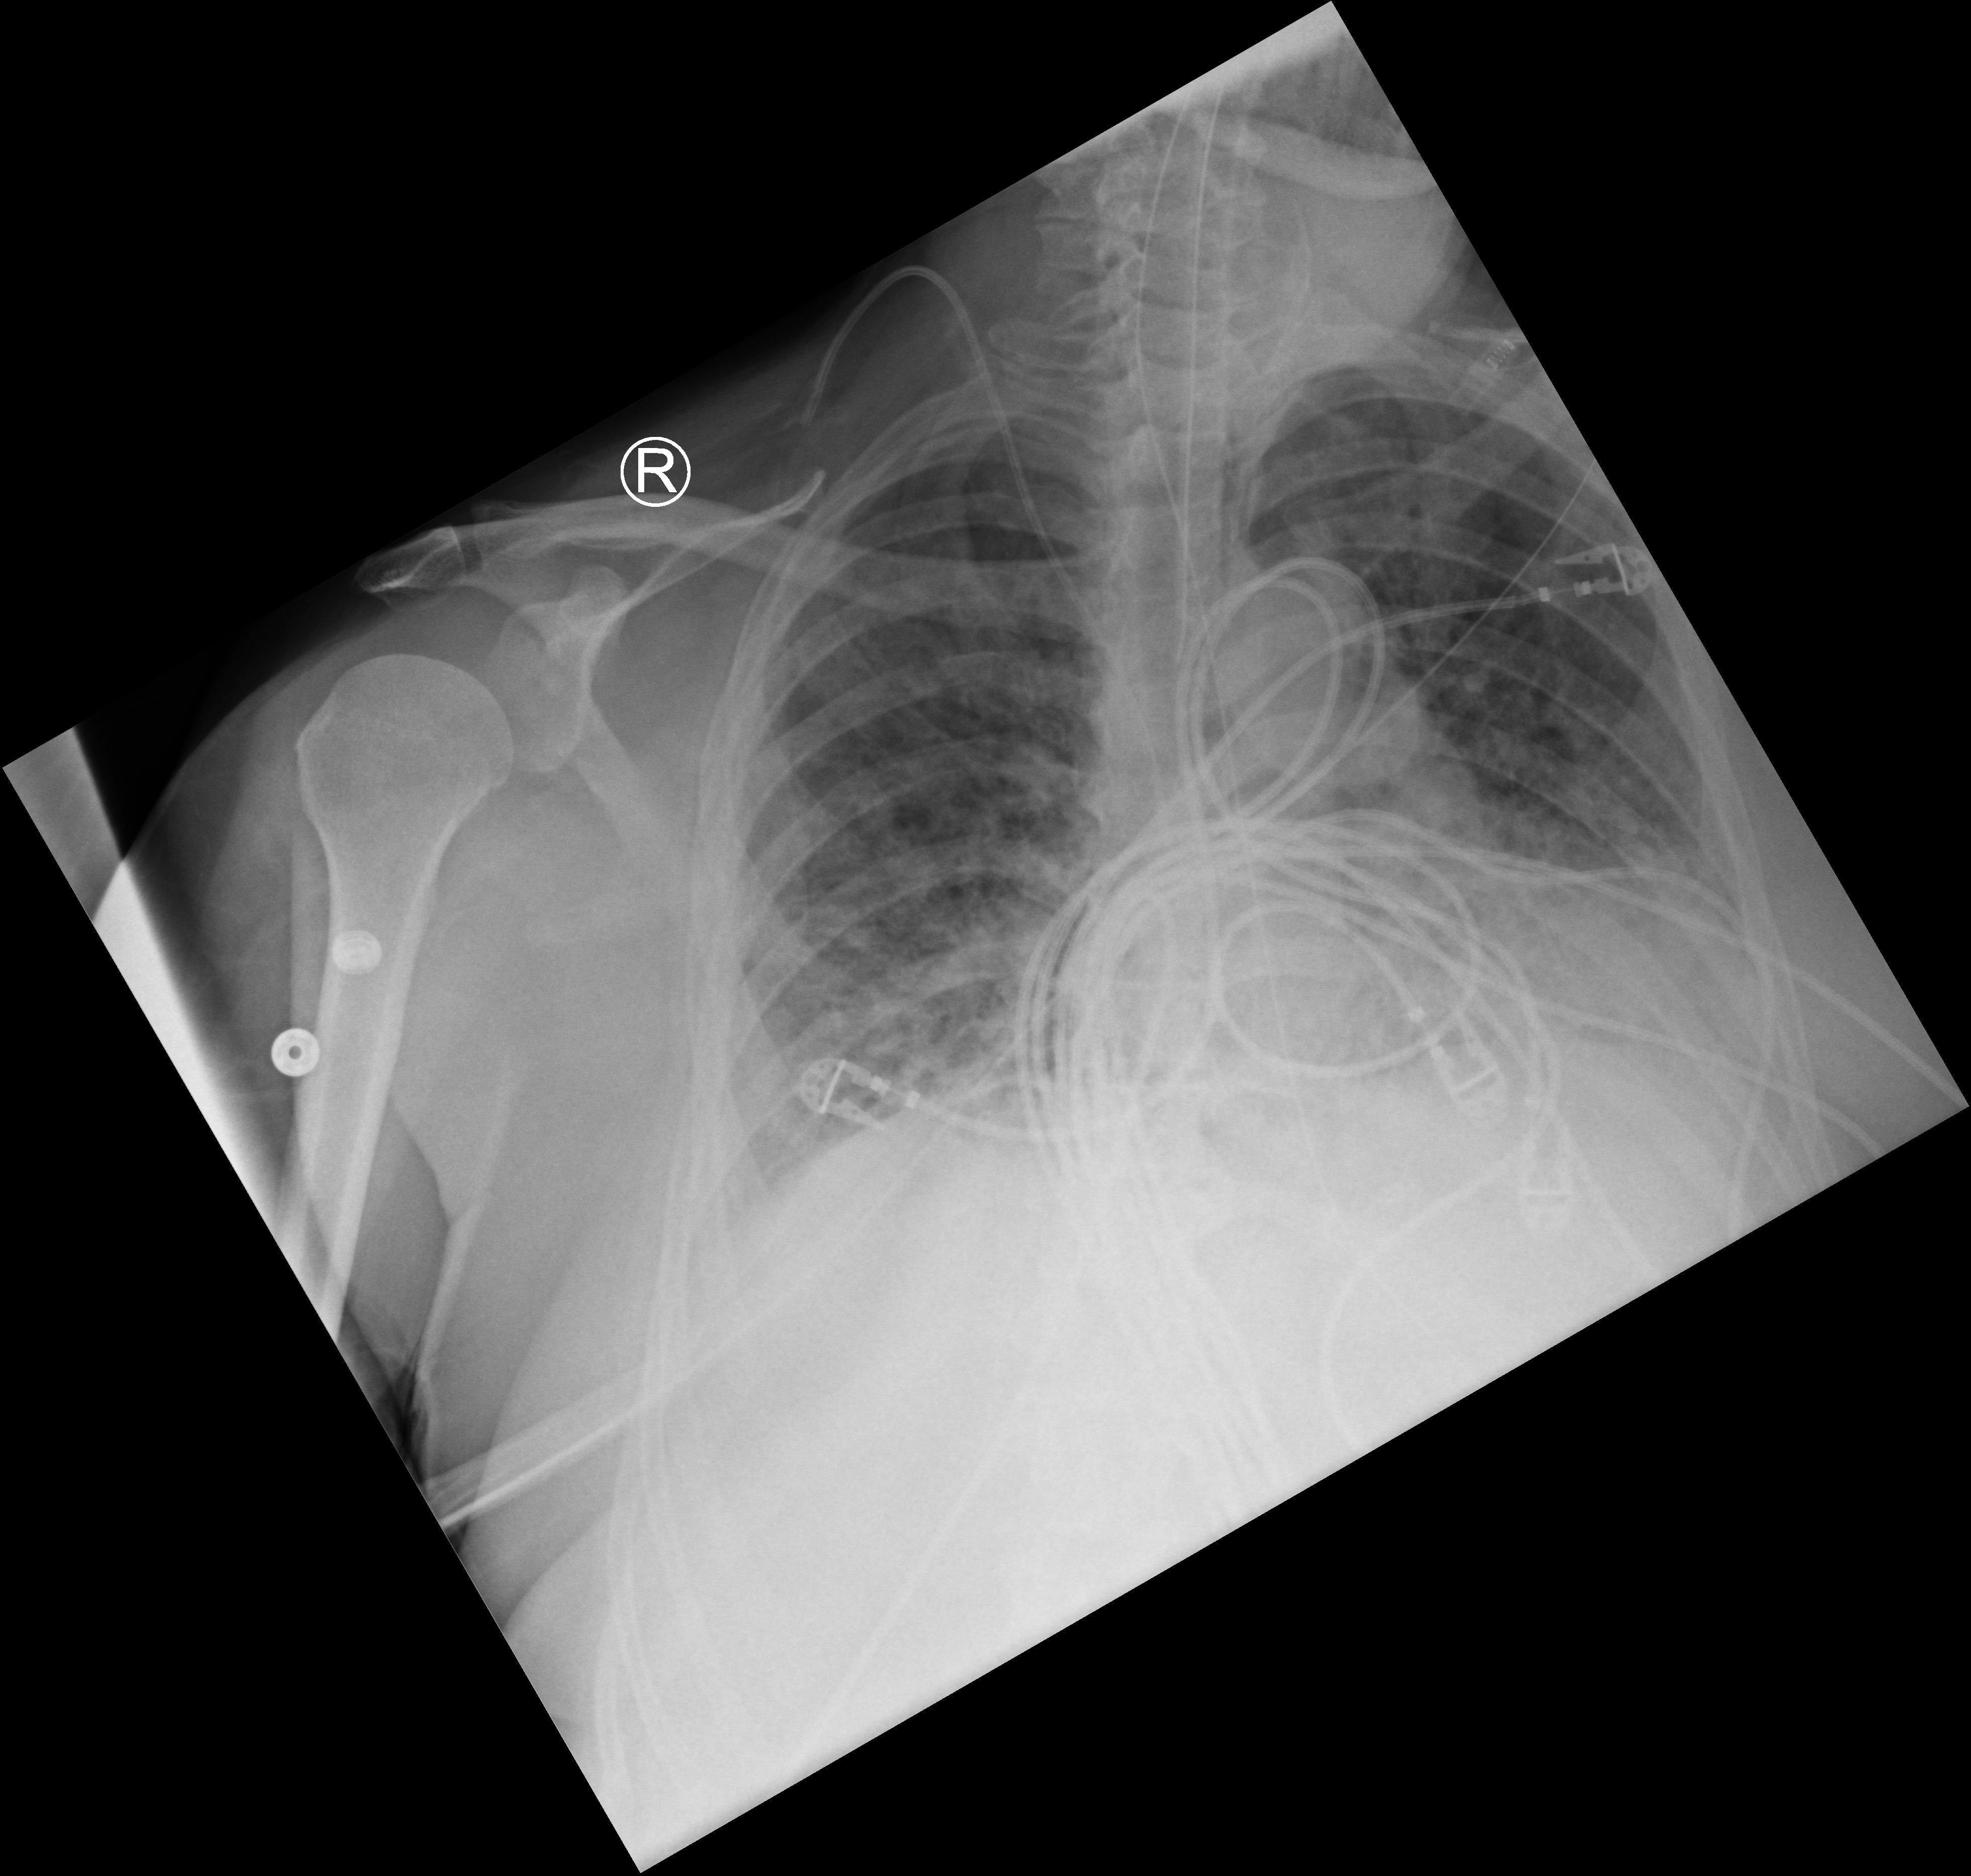
Chest X-ray (portable), anteroposterior (AP) projection. Male patient hospitalised with COVID-19, age 60–74 years.
Hospital-stay facts (about this admission, not read from this image; timing relative to this image not recorded): mechanically ventilated during this hospital stay: yes.